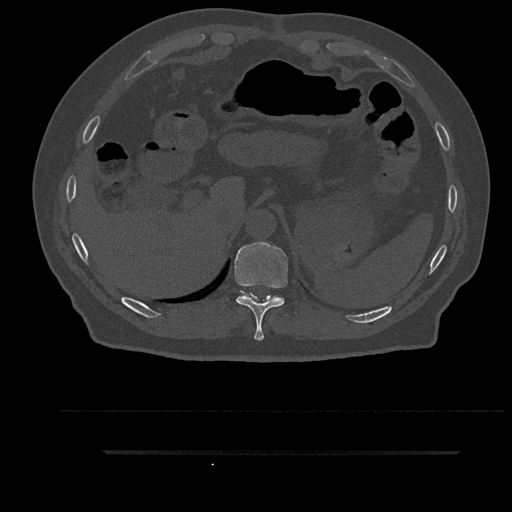
CT including the spine, one axial slice. Position 351 of 797 along the scan axis. Reconstruction kernel Br40s/3. 120 kVp. Bone window (W 1800 / L 400 HU). 512 × 512 image matrix, field of view 432 × 432 mm. Male patient, age 63 years. From the clinical record (not read from this slice): primary cancer: renal; vertebrae with lytic lesions (as recorded): T8.
Annotated regions visible in this slice (semi-automatic segmentation, software-assisted and operator-edited):
- T10 vertebra: bounding box <235,242,288,341> (left, top, right, bottom; pixels)
- T11 vertebra: <240,291,280,299>